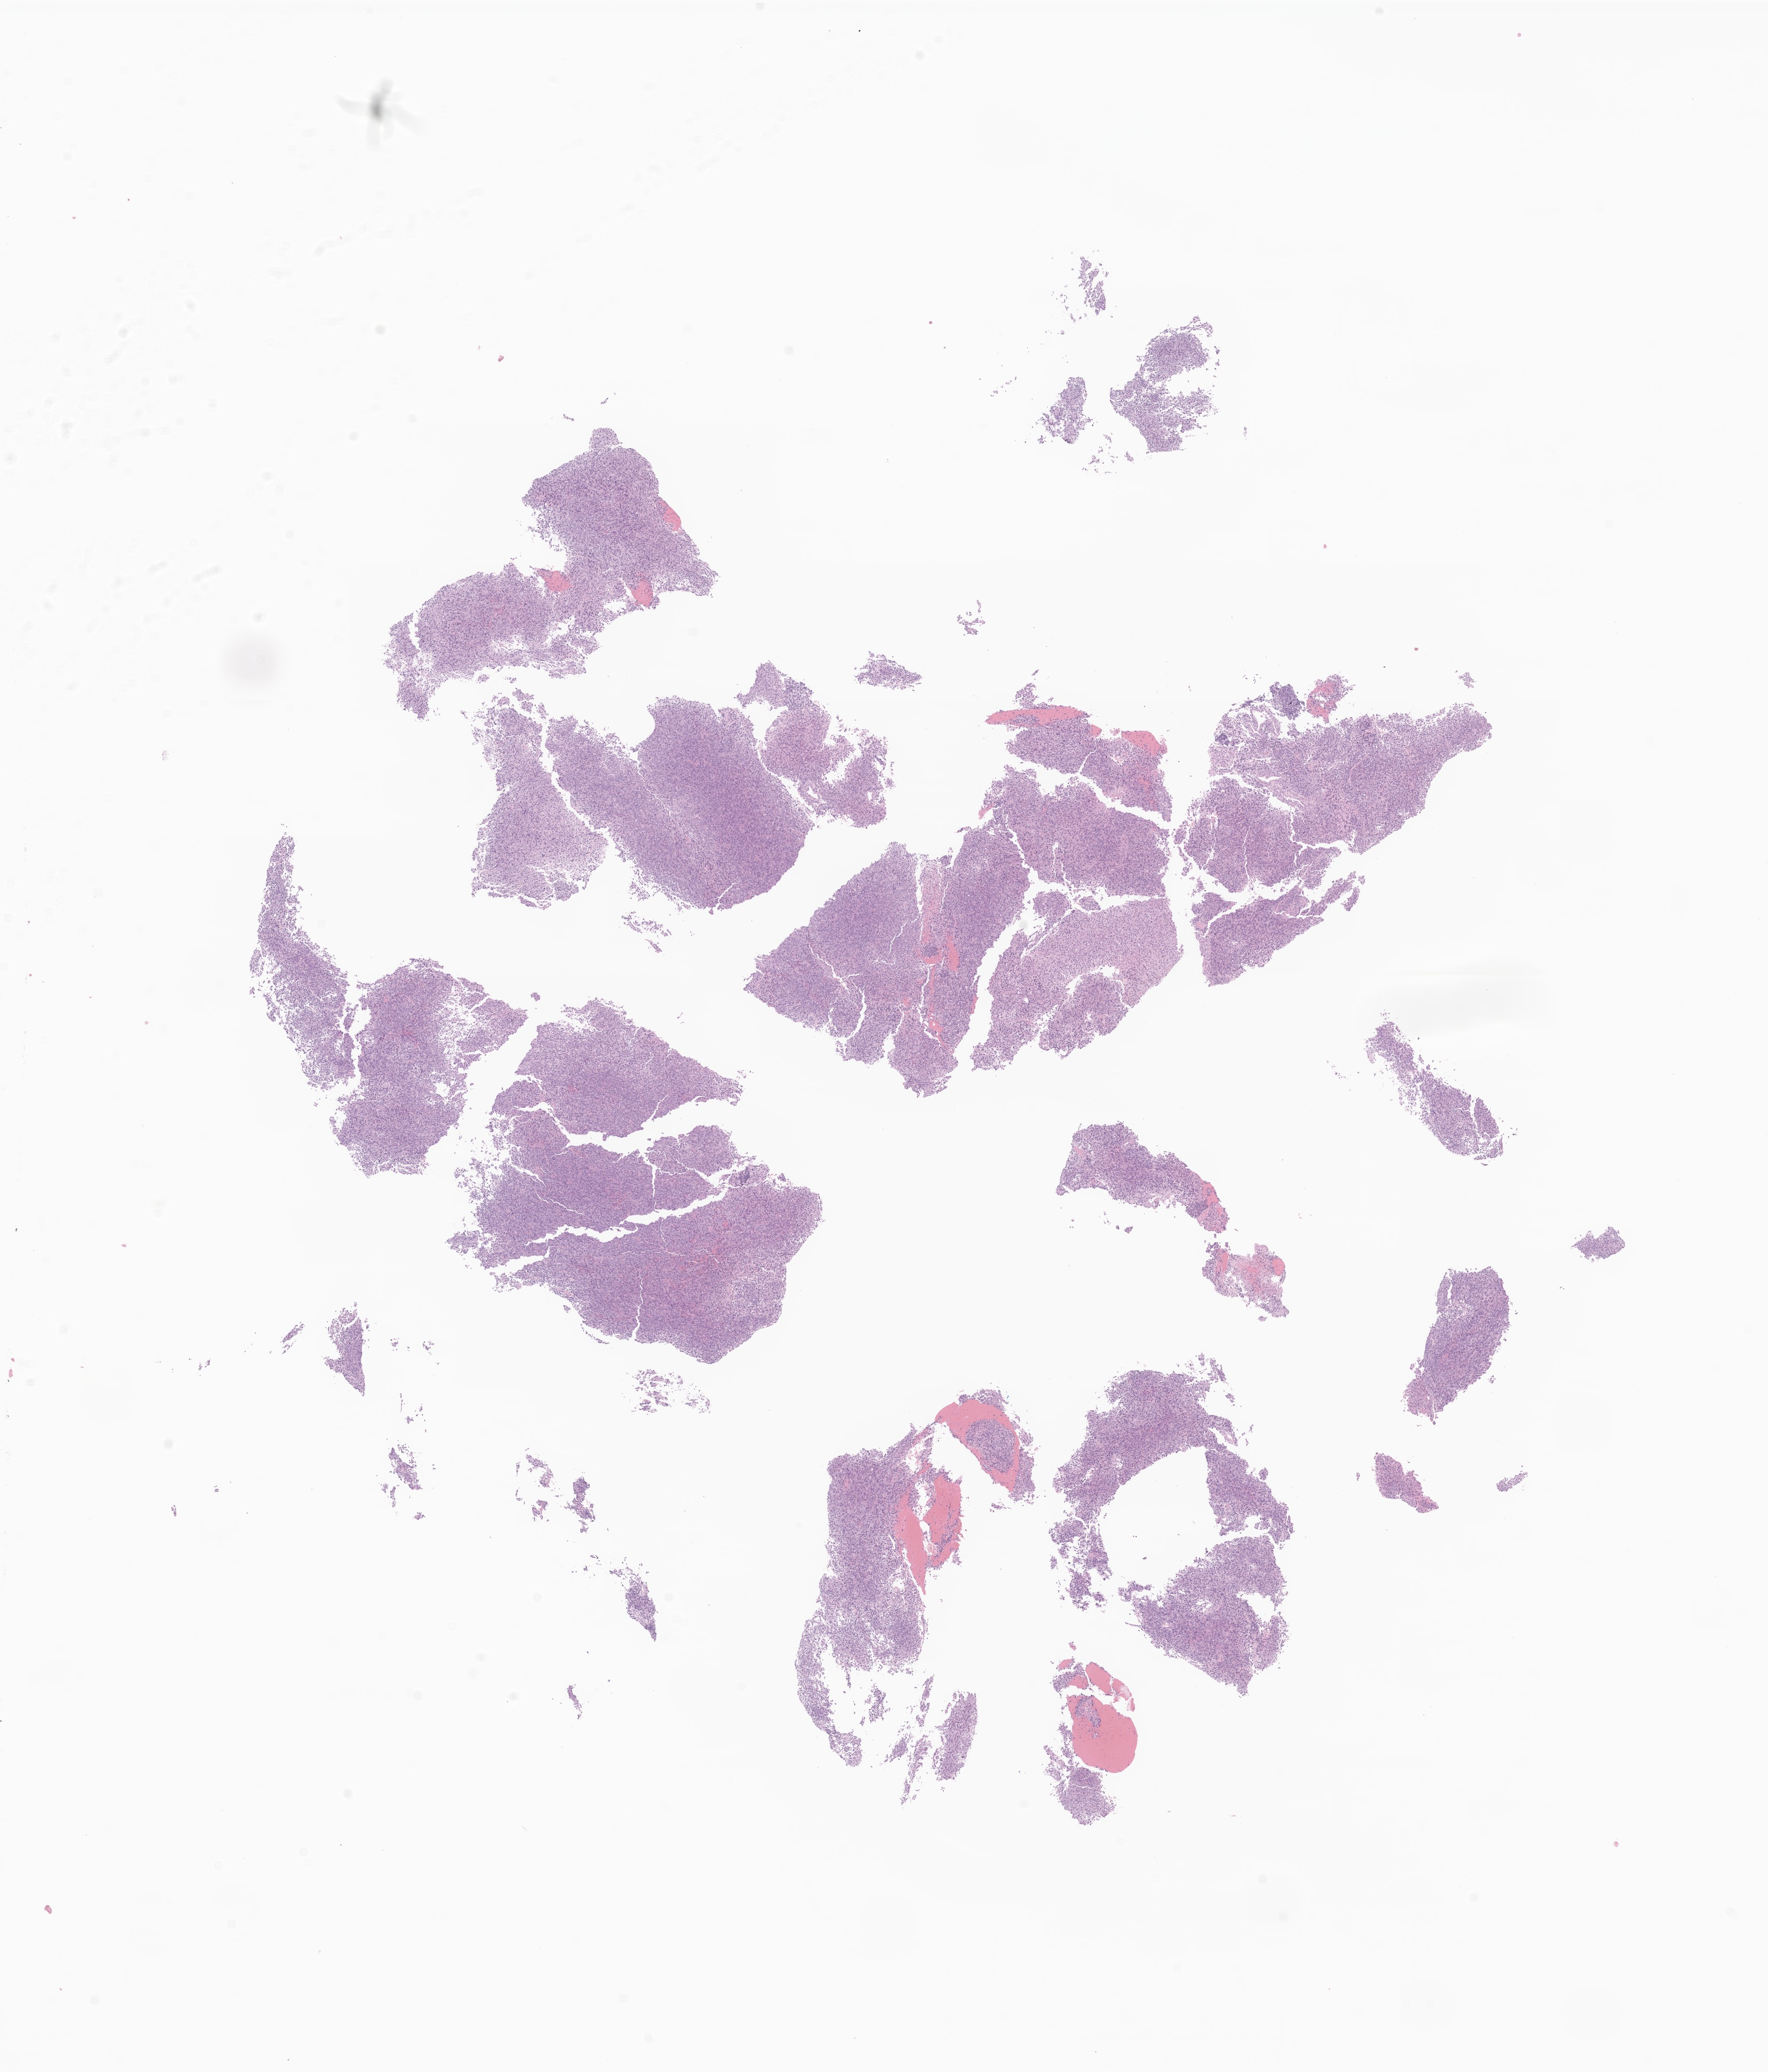
Digitized hematoxylin and eosin (H&E)-stained section of tumor tissue from the brain — shown as a low-resolution overview of the whole scanned area (about 13.7 x 16.1 mm), formalin-fixed, paraffin-embedded (FFPE) tissue. Patient male; age 149 months (12 years 5 months).
Recorded diagnosis: Neoplasm, malignant, uncertain whether primary or metastatic.